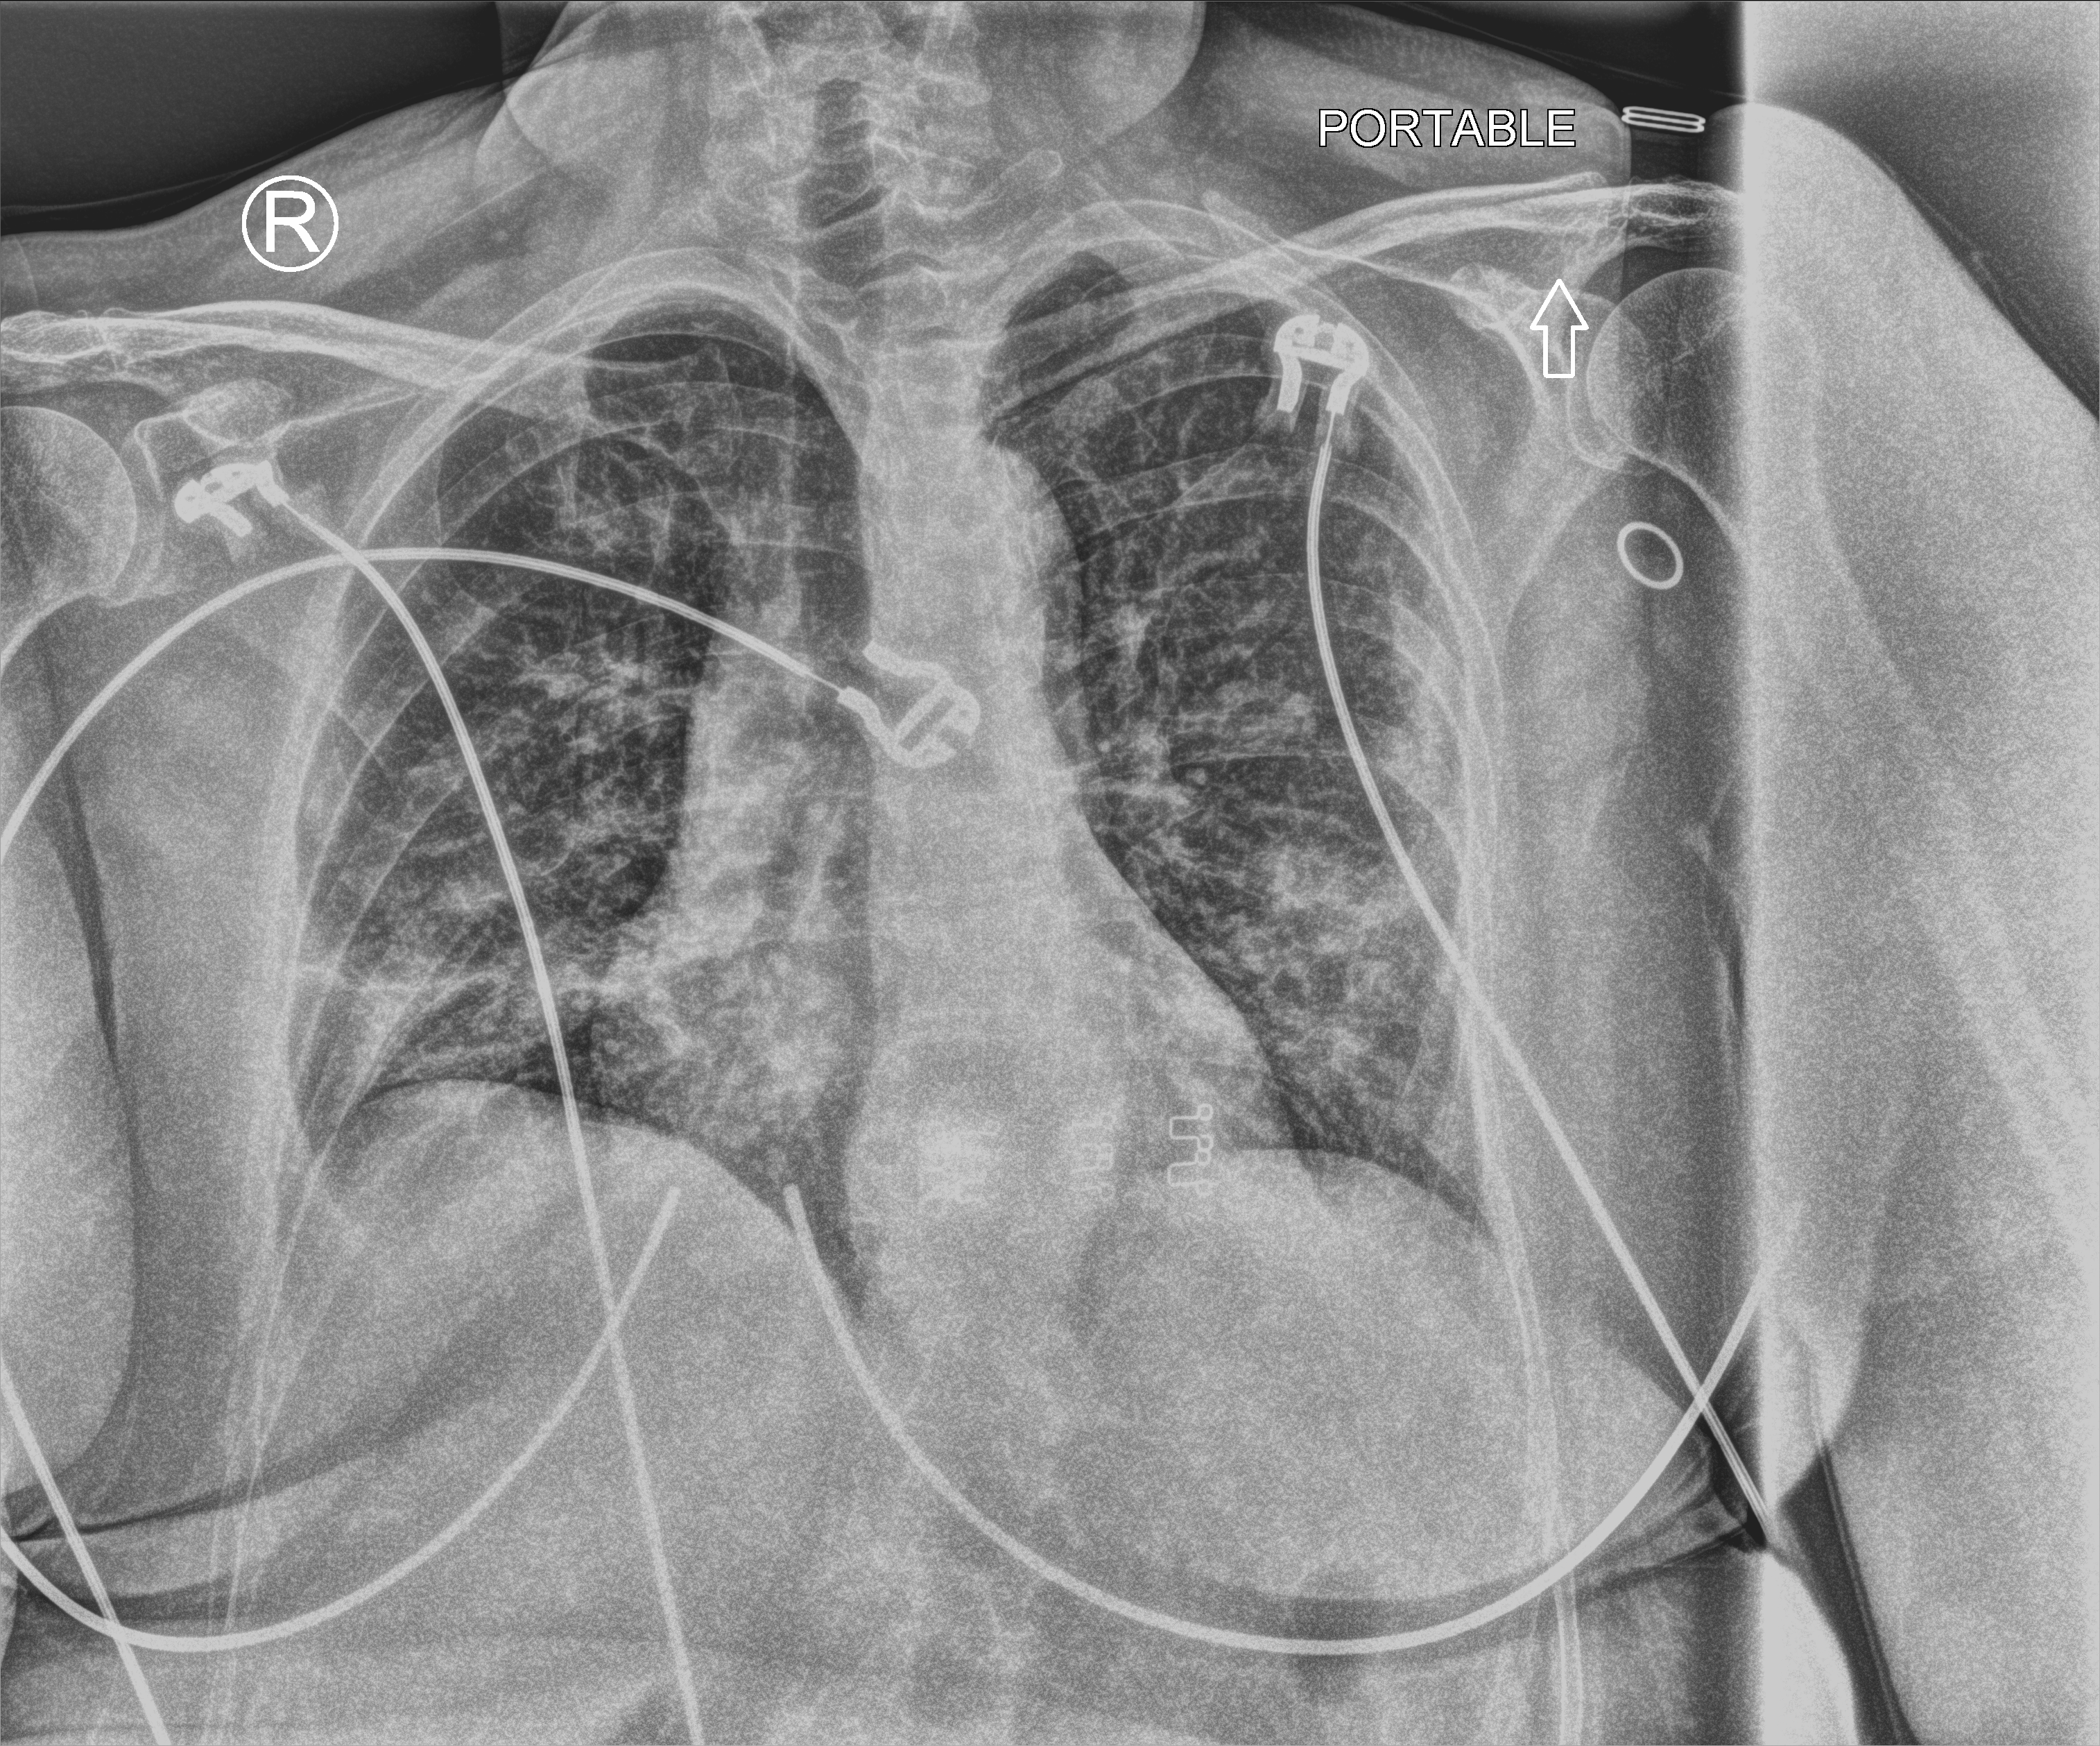
Chest X-ray (portable), anteroposterior (AP) projection. Patient hospitalised with COVID-19; female, aged 60–74 years.
From the hospital-stay record, not from the radiograph (when in the stay this image was taken is not recorded):
- chronic kidney disease (admission record): no
- admitted to intensive care during this hospital stay: no
- hypertension (admission record): yes